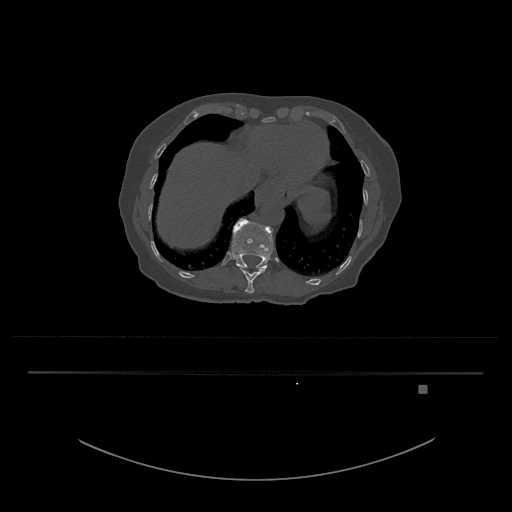
CT including the spine, one axial slice. Reconstruction kernel Br40s/3. 120 kVp. Bone window (W 1800 / L 400 HU). 512 × 512 image matrix. Patient: female, 57 years. Case-level facts recorded for this patient, not image findings: primary cancer: cervical.
Annotated regions visible in this slice (semi-automatic segmentation, software-assisted and operator-edited):
- T11 vertebra: bounding box [x1, y1, x2, y2] px = [238, 266, 266, 293]
- T12 vertebra: [231, 218, 273, 269]